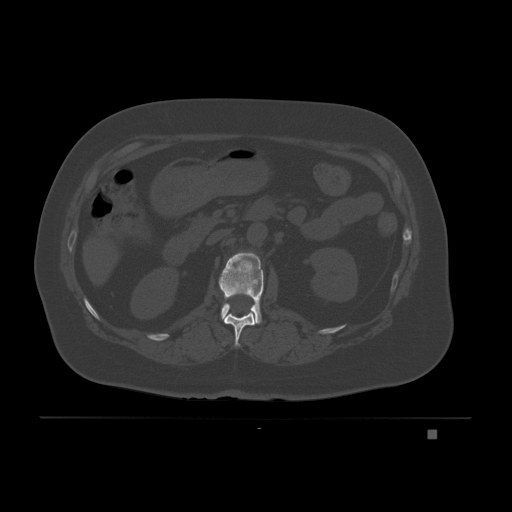
CT including the spine, one axial slice. Position 75 of 221 along the scan axis. Bone window (W 1800 / L 400 HU). 3 mm slice thickness. 512 × 512 image matrix, field of view 474 × 474 mm. Female patient, age 63 years. From the clinical record (not read from this slice): primary cancer: breast.
Annotated regions visible in this slice (semi-automatically segmented with operator editing):
- L1 vertebra: bounding box [x1, y1, x2, y2] px = [218, 252, 264, 324]
- T12 vertebra: [224, 311, 256, 347]